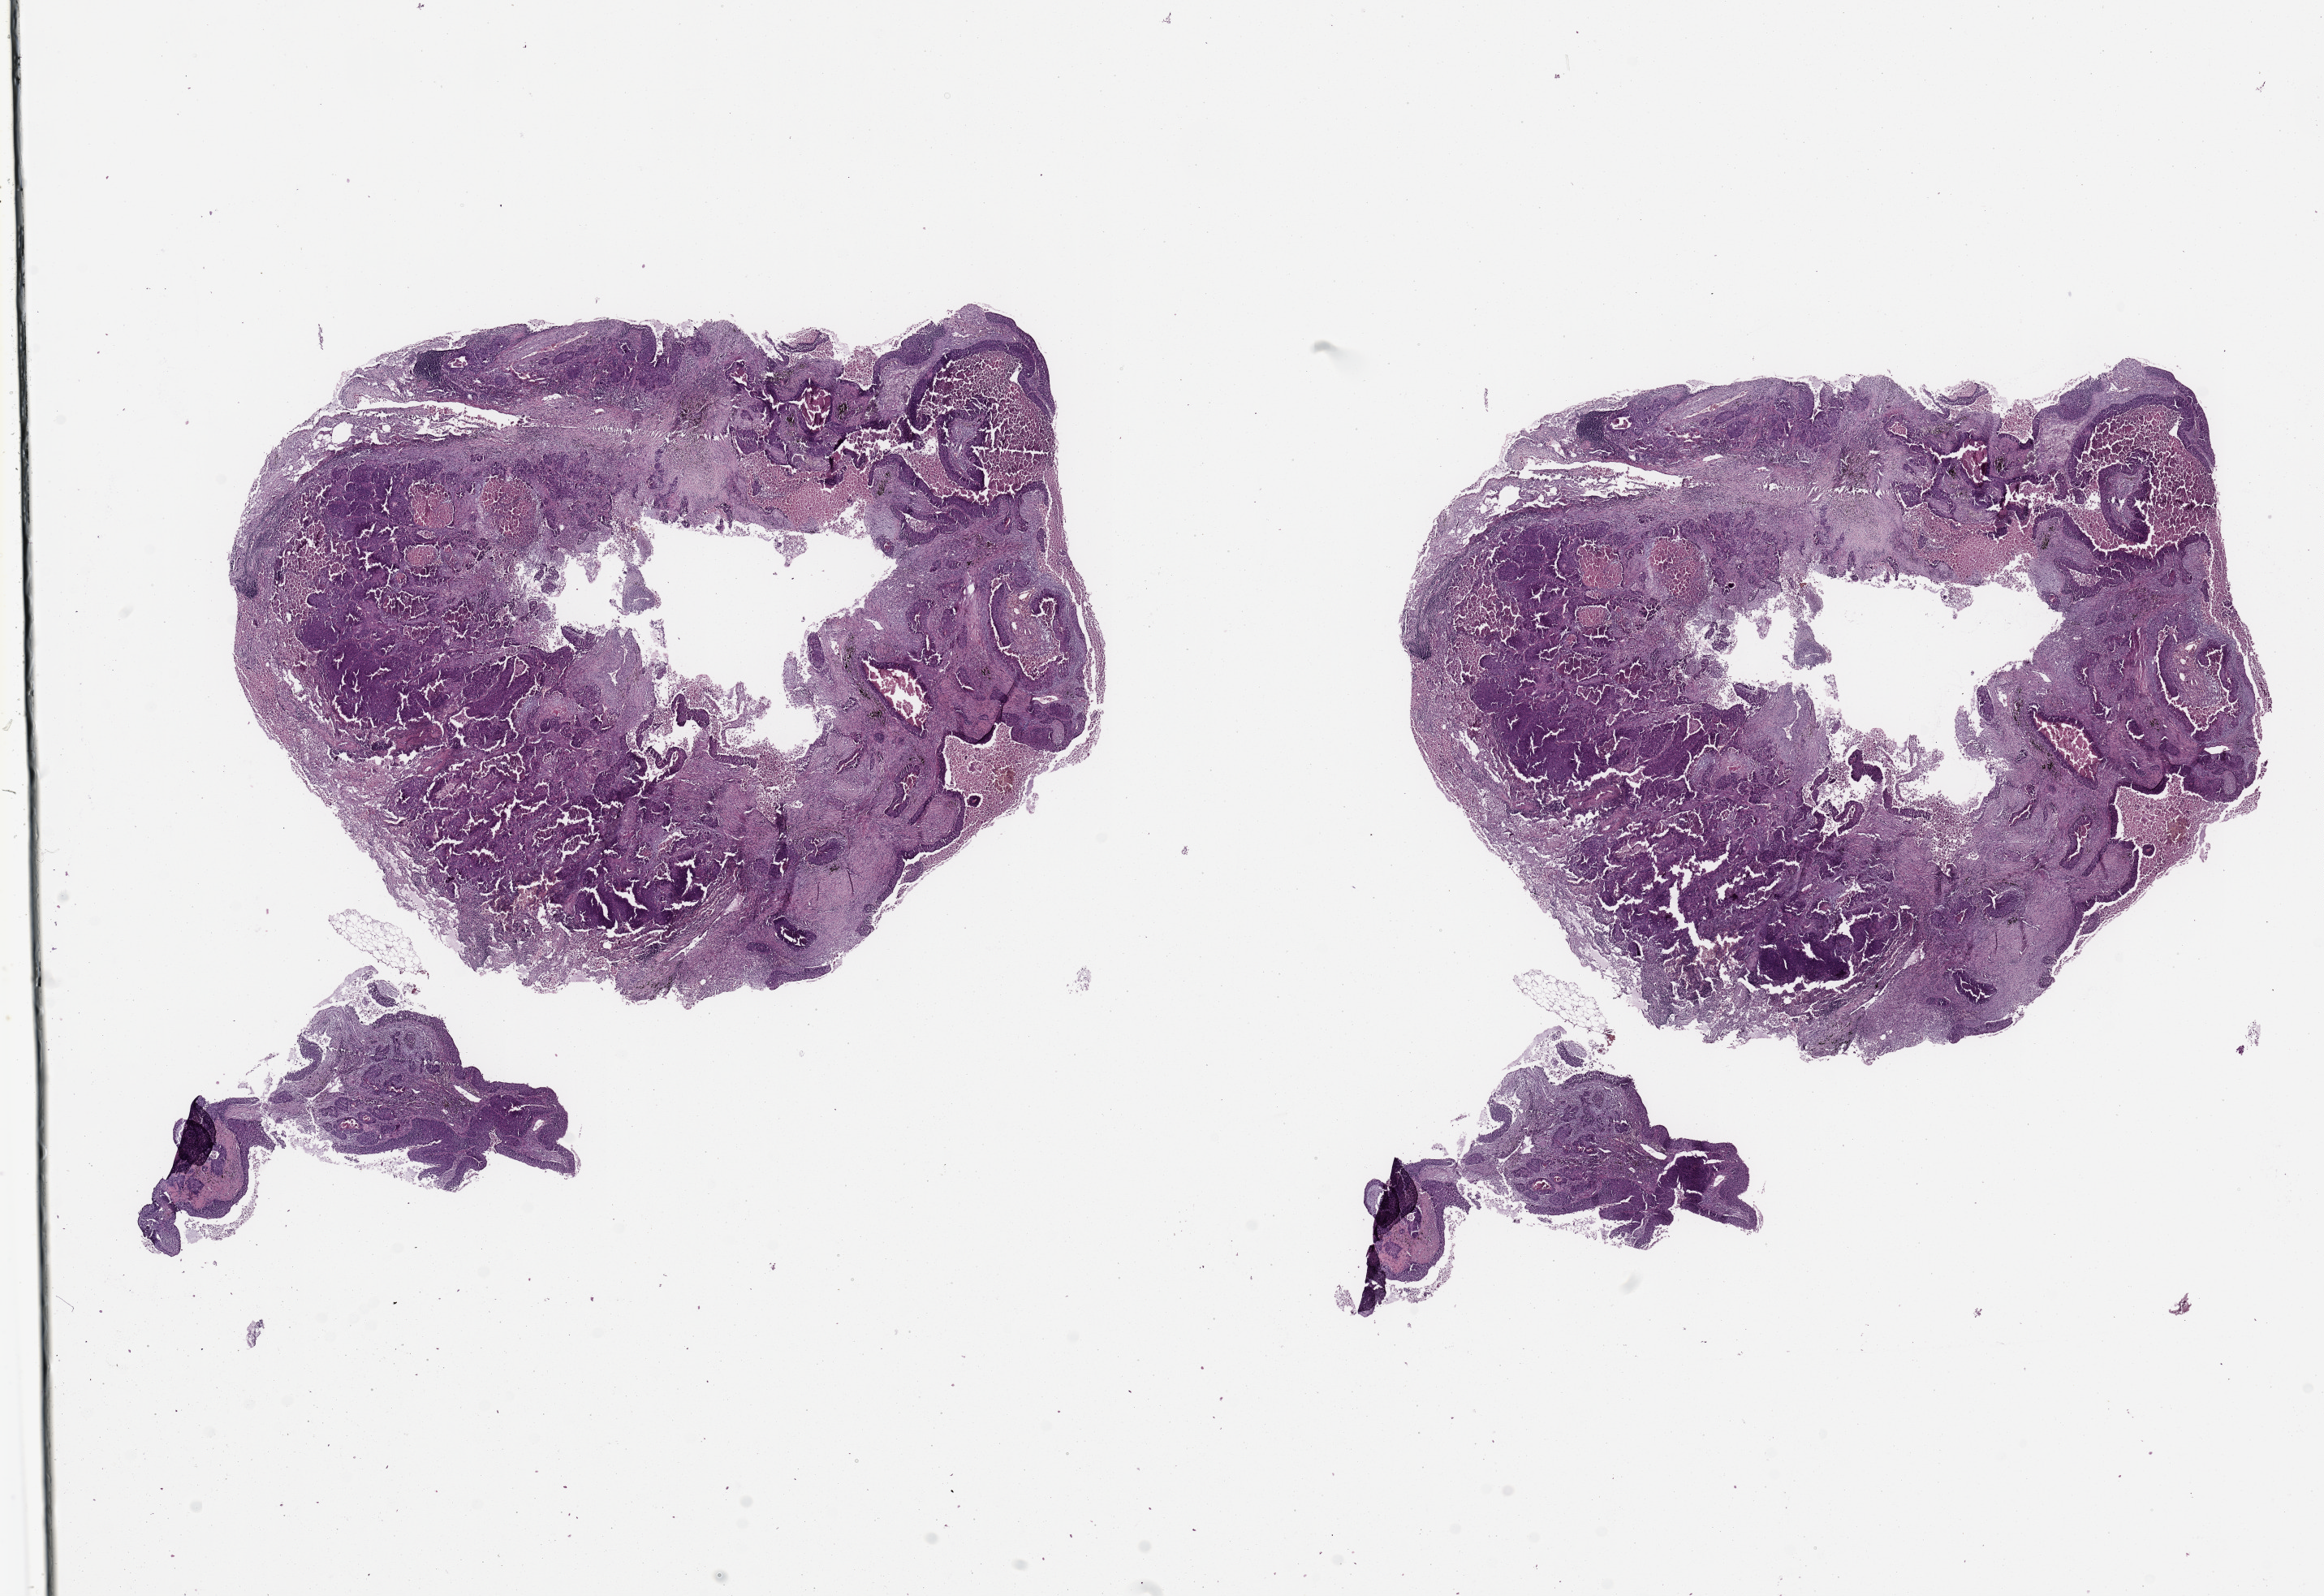
H&E whole-slide image, a low-resolution overview of the entire scanned area, about 22.6 x 15.5 mm (acquisition: 20x scan). Tumour tissue sample, sampled site: lung. Male, 76 y/o. Histologic grade: G2 (moderately differentiated). Composition of this section per pathologist review: tumour nuclei 65%, necrosis 15%.
Histologic diagnosis: Squamous cell carcinoma, NOS. Primary tumour site (as recorded): right middle lobe. AJCC pathologic stage: IA.